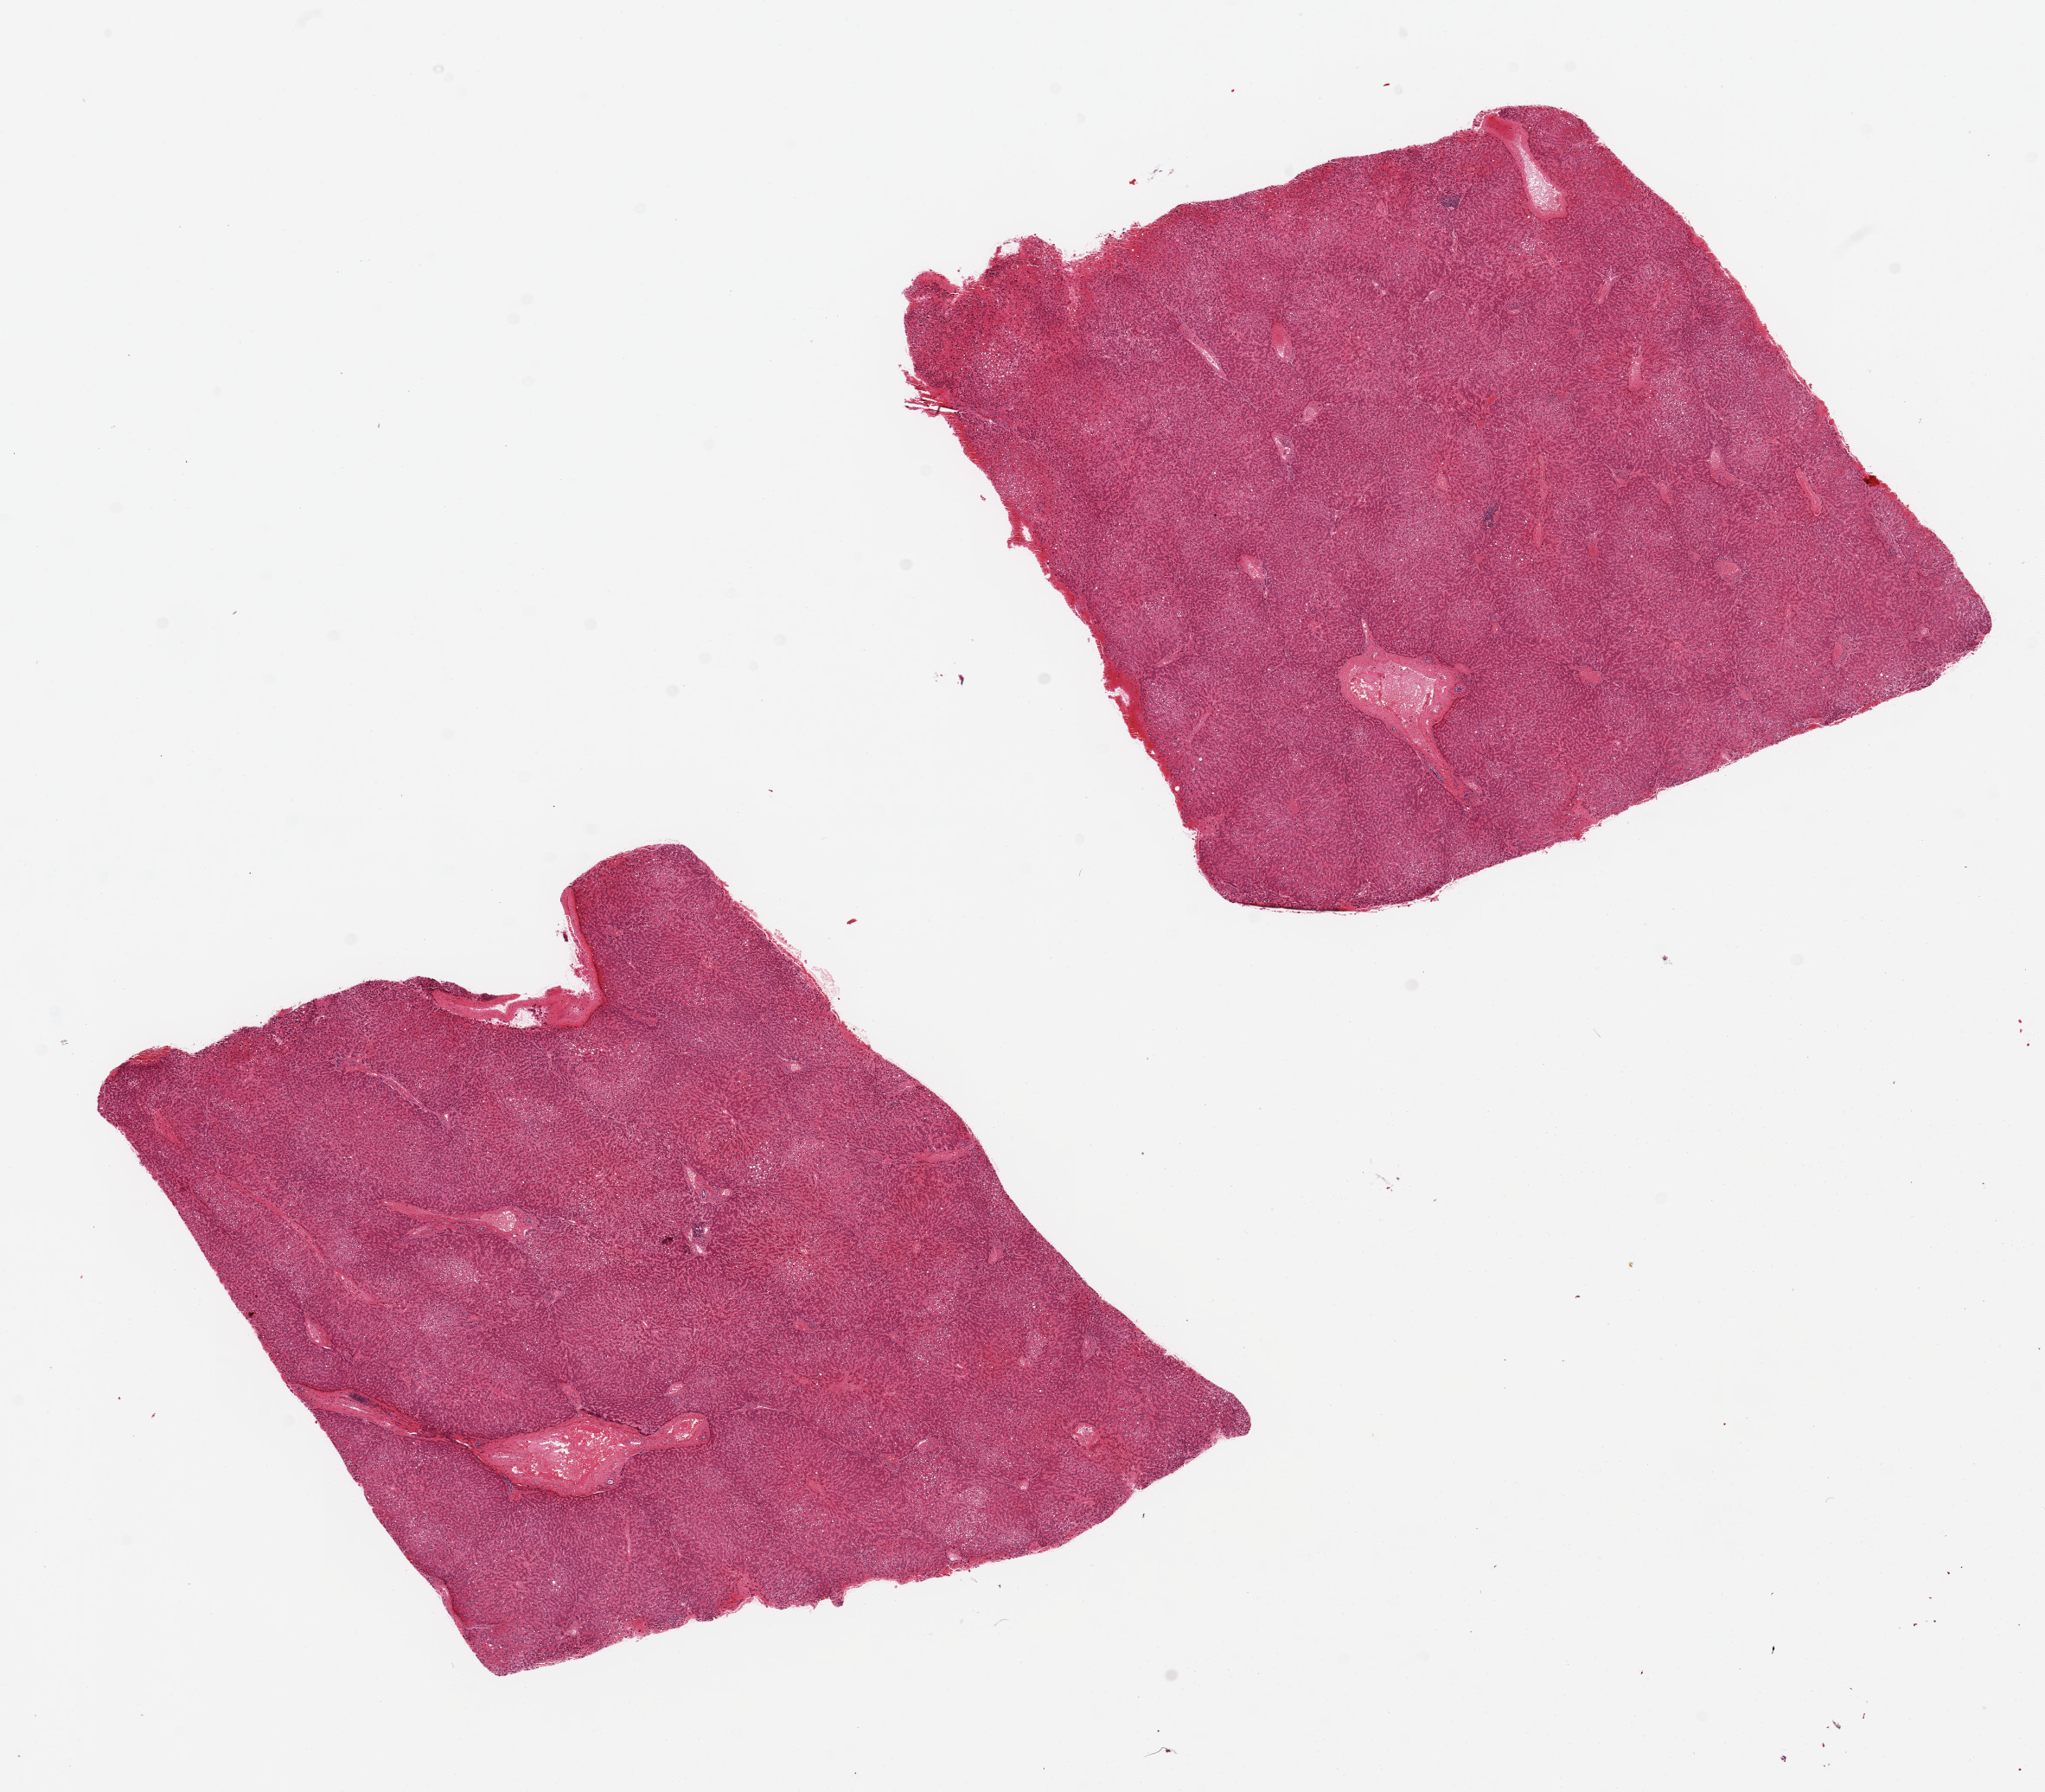
H&E whole-slide image, whole scanned area (about 18.7 x 16.4 mm) shown as a low-resolution overview. PAXgene-fixed, paraffin-embedded tissue. Sampled site (target tissue): liver. Donor tissue sample. Donor: male.
Reviewer comment on this tissue sample: 2 pieces, steatosis, congestion.